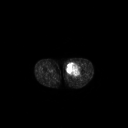
FDG PET of an extremity soft-tissue mass (from a PET/CT study), one axial slice; slice 234 of 267 in the series (ordered by position); 3.27 mm slice thickness; 128 × 128 image matrix, field of view 700 × 700 mm. Patient: male, 63 years. From the clinical record (not read from this slice): histological type: pleiomorphic liposarcoma; grade: high; site of the primary tumour: left thigh.
Outlined on this slice (expert contour drawn on MRI and transferred to this co-registered scan by the dataset authors):
- gross tumour volume including surrounding oedema: bounding box (x1, y1, x2, y2) in pixels: (66, 62, 81, 76)
- gross tumour volume (mass): (66, 63, 79, 75)